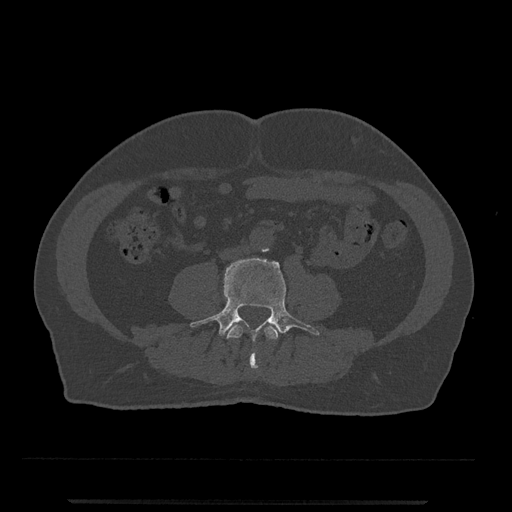
CT including the spine, one axial slice. Reconstruction kernel Br40s/3. 120 kVp. Bone window (W 1800 / L 400 HU). 0.5 mm slice thickness. 512 × 512 image matrix, field of view 419 × 419 mm. Male patient, age 63 years. From the clinical record (not read from this slice): primary cancer: prostate.
Annotated regions visible in this slice (semi-automatic segmentation, software-assisted and operator-edited):
- L3 vertebra: bounding box (x1, y1, x2, y2) in pixels: (226, 324, 280, 370)
- L4 vertebra: (189, 257, 320, 365)